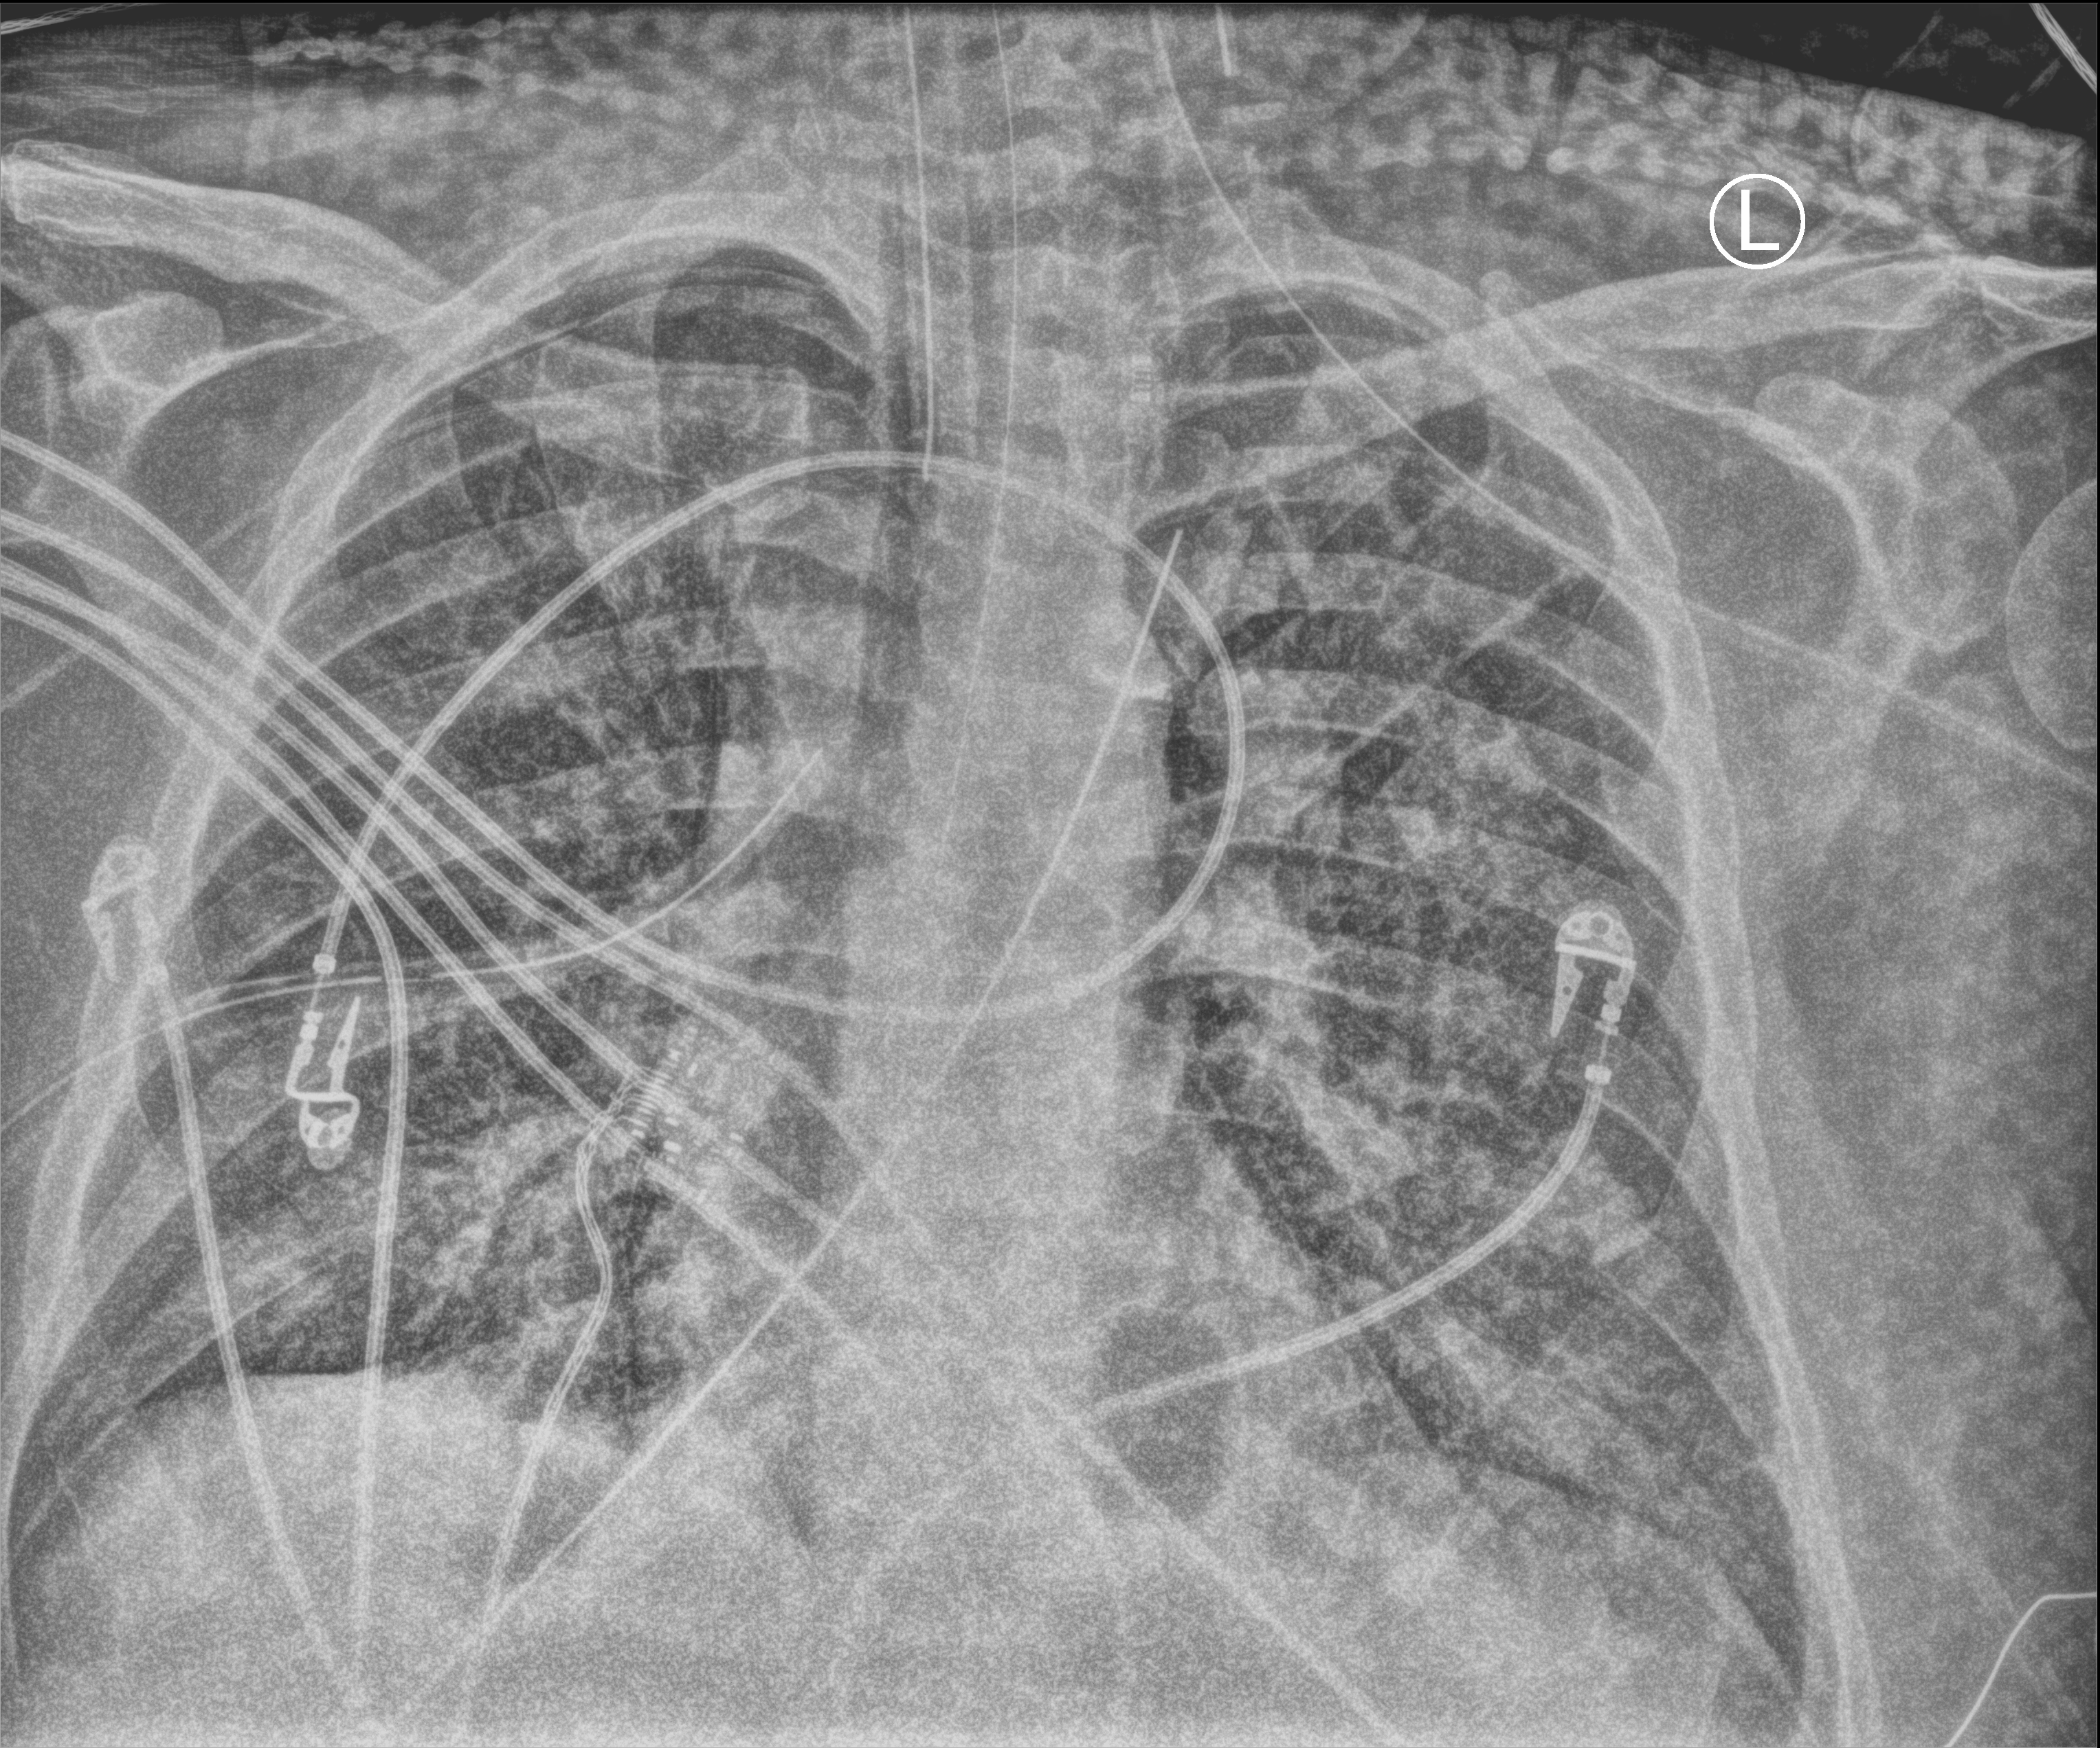
Portable chest radiograph, anteroposterior (AP) projection. Adult patient hospitalised with COVID-19, age 18–59 years.
Admission-level facts for this patient (not findings on this image; timing relative to this image not recorded):
- admitted to intensive care during this hospital stay: yes
- mechanically ventilated during this hospital stay: yes
- hypertension (admission record): yes